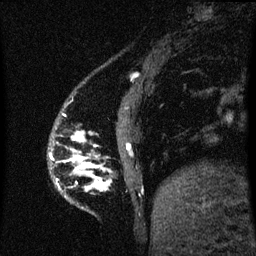
Breast MRI (dynamic contrast-enhanced), one sagittal slice; position 9 of 60 along the scan axis; dynamic contrast-enhanced series, image 2 of 3 at this slice position (ordered by acquisition); 1.5 T; TE 4.2 ms, TR 8 ms; 256 × 256 image matrix. Patient: female, 50 years.
Outlined on this slice (semi-automatic segmentation, software-assisted and operator-edited):
- analysis volume of interest (the breast-tissue region the enhancement analysis was run in; not a lesion): box from (x=74, y=132) to (x=107, y=183) px
- tumour enhancement mask (voxels above the 70 % enhancement threshold inside the analysis volume of interest): (x=78, y=136)–(x=82, y=138)